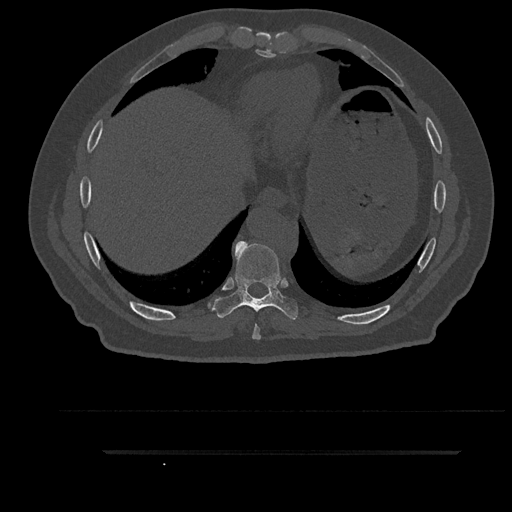
CT including the spine, one axial slice. Reconstruction kernel Br40s/3. 120 kVp. Bone window (W 1800 / L 400 HU). 512 × 512 image matrix. Patient: male, 63 years. Case-level facts recorded for this patient, not image findings: primary cancer: renal; vertebrae with lytic lesions (as recorded): T8.
Outlined on this slice (semi-automatically segmented with operator editing):
- T8 vertebra: bounding box (x1, y1, x2, y2) in pixels: (252, 325, 261, 340)
- T9 vertebra: (212, 241, 298, 320)